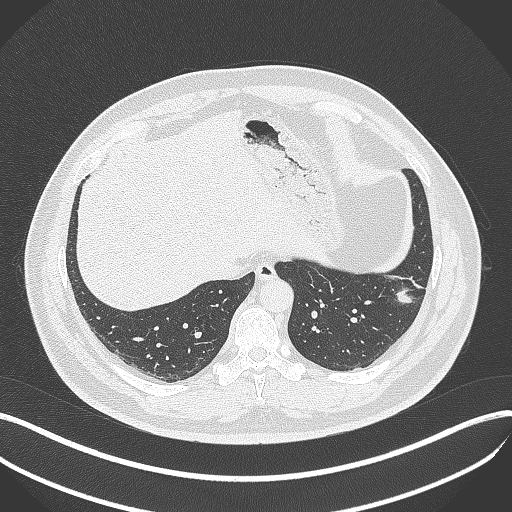
Chest CT, one axial slice; position 108 of 429 along the scan axis; reconstruction kernel B70f; lung window (W 1500 / L -600 HU); 1 mm slice thickness; 512 × 512 image matrix, field of view 400 × 400 mm. Patient: male, 39 years. From the clinical record (not read from this slice): clinical TNM (as recorded): T2a N0 M0.
Annotated regions visible in this slice (rectangle marked by the reading radiologist):
- lung tumour (recorded histology: adenocarcinoma): bounding box [x1, y1, x2, y2] px = [391, 280, 418, 305]